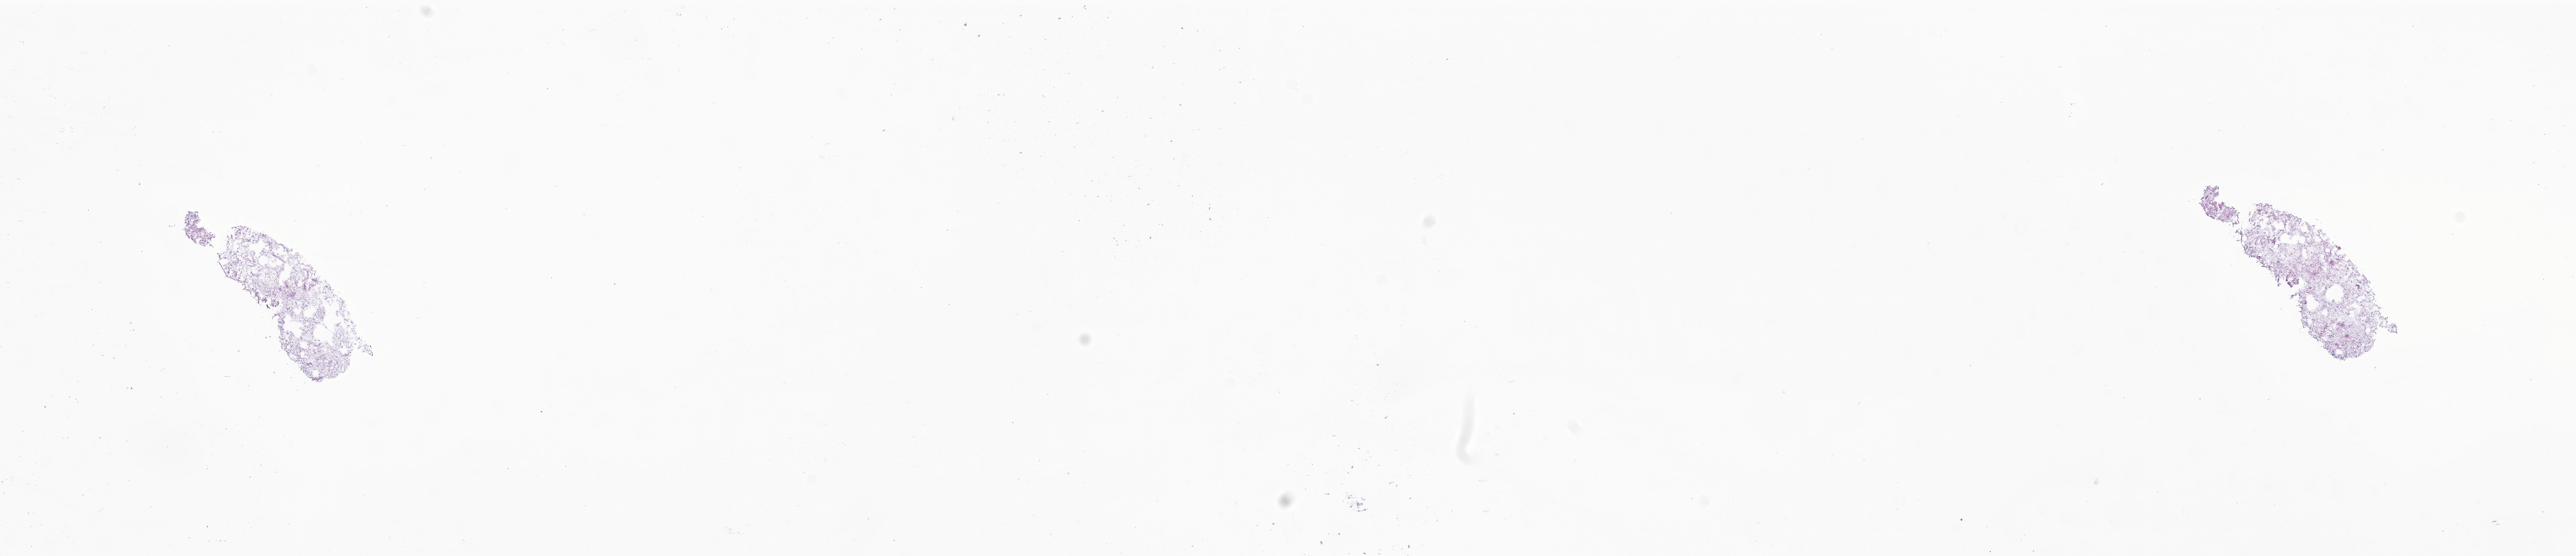
Whole-slide image, H&E stain of tumor tissue from the cerebellum, low-resolution overview of the scanned area, about 26.6 x 5.7 mm. Cryosection (OCT / tissue freezing medium). Patient female; age 78 months (6 years 6 months).
• recorded diagnosis: Ganglioglioma, NOS